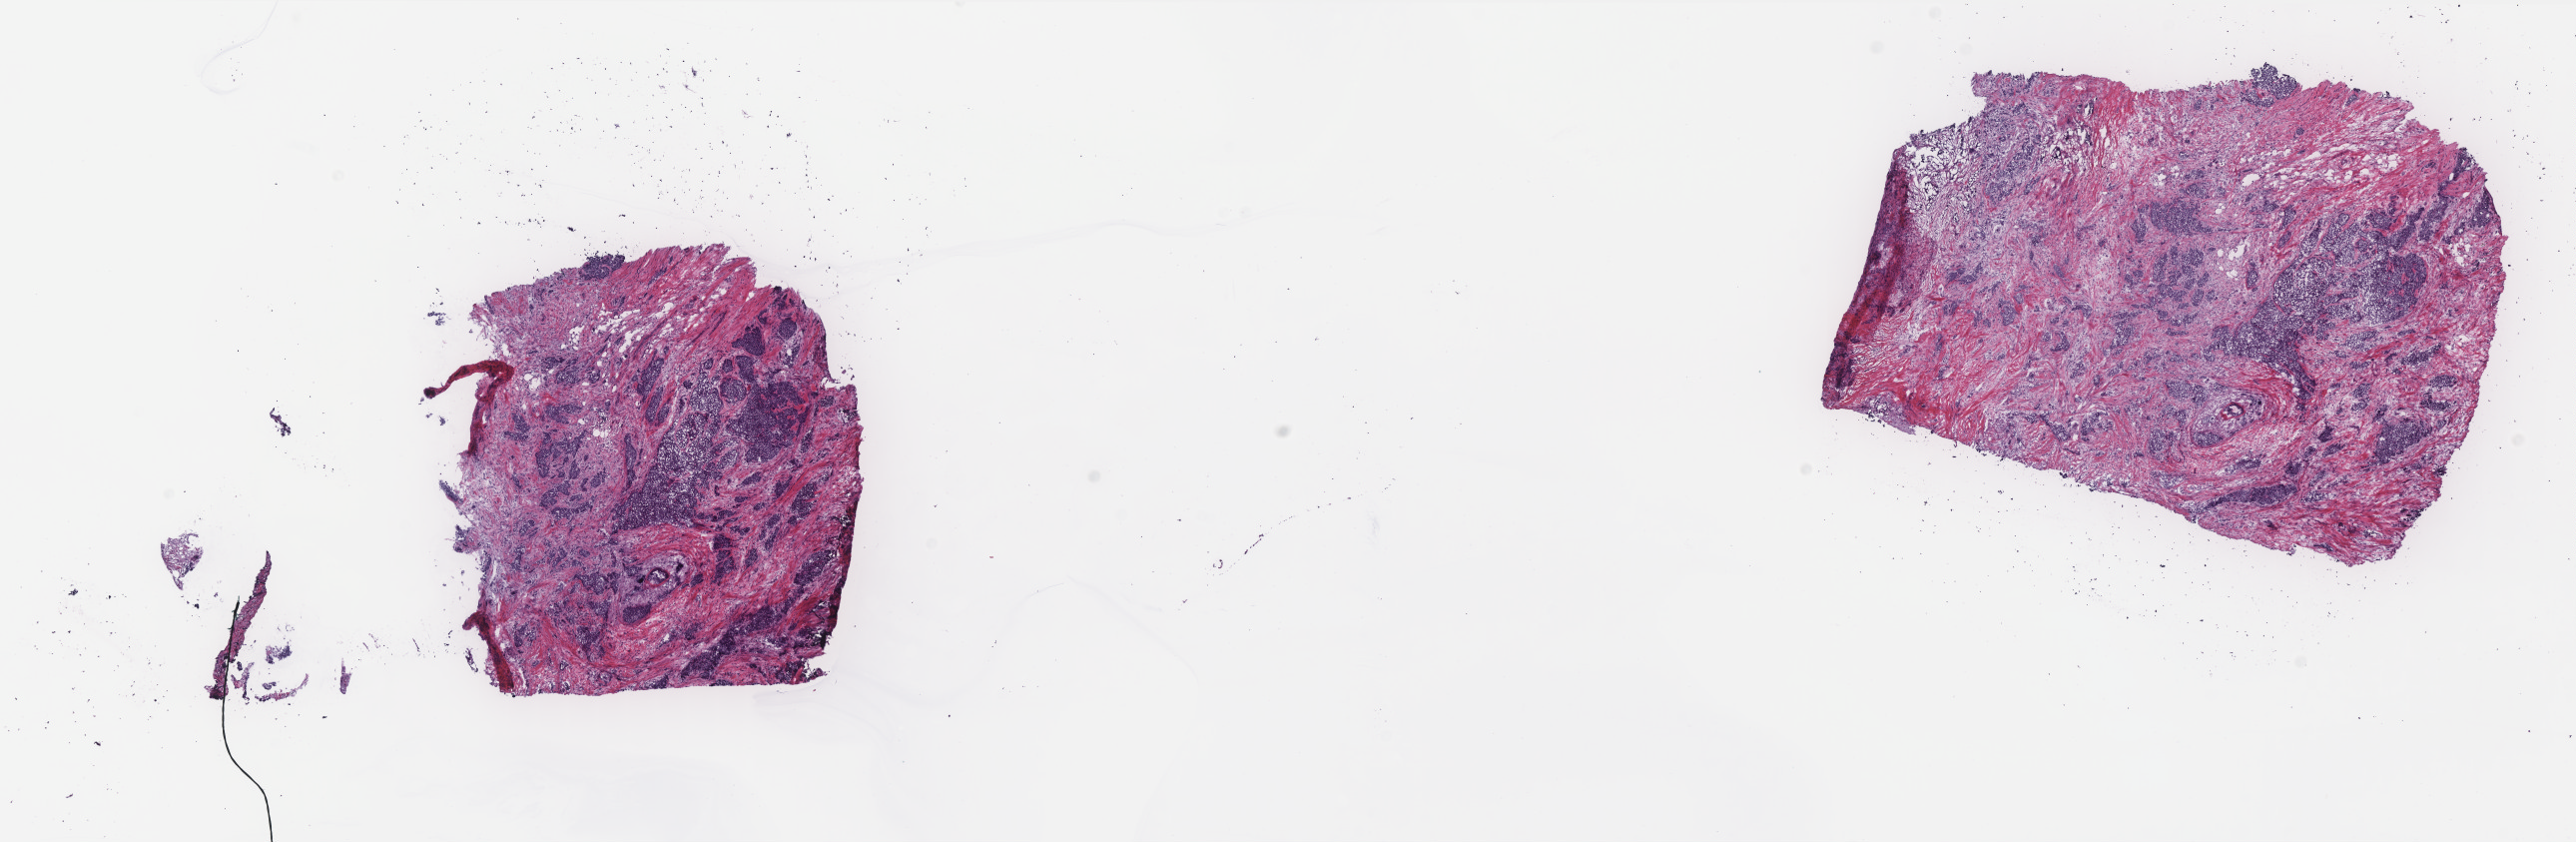
Hematoxylin and eosin (H&E) stained whole-slide image — whole scanned area (about 20.7 x 6.8 mm, acquisition: 40x scan) shown as a low-resolution overview; frozen section from the top of the tissue portion; breast, primary tumour sample. Patient: female, age at initial diagnosis 73 years. Pathologist review of this section (percent, as recorded): tumour cells 75%, tumour nuclei 75%, normal cells 1%, stromal cells 24%, necrosis 0%. Inflammatory infiltration, as recorded: lymphocyte infiltration 3%, monocyte infiltration 1%, neutrophil infiltration 1%.
• AJCC pathologic stage: IA (7th edition)
• TNM: T1c N0 M0
• pathologic diagnosis: Infiltrating duct carcinoma, NOS